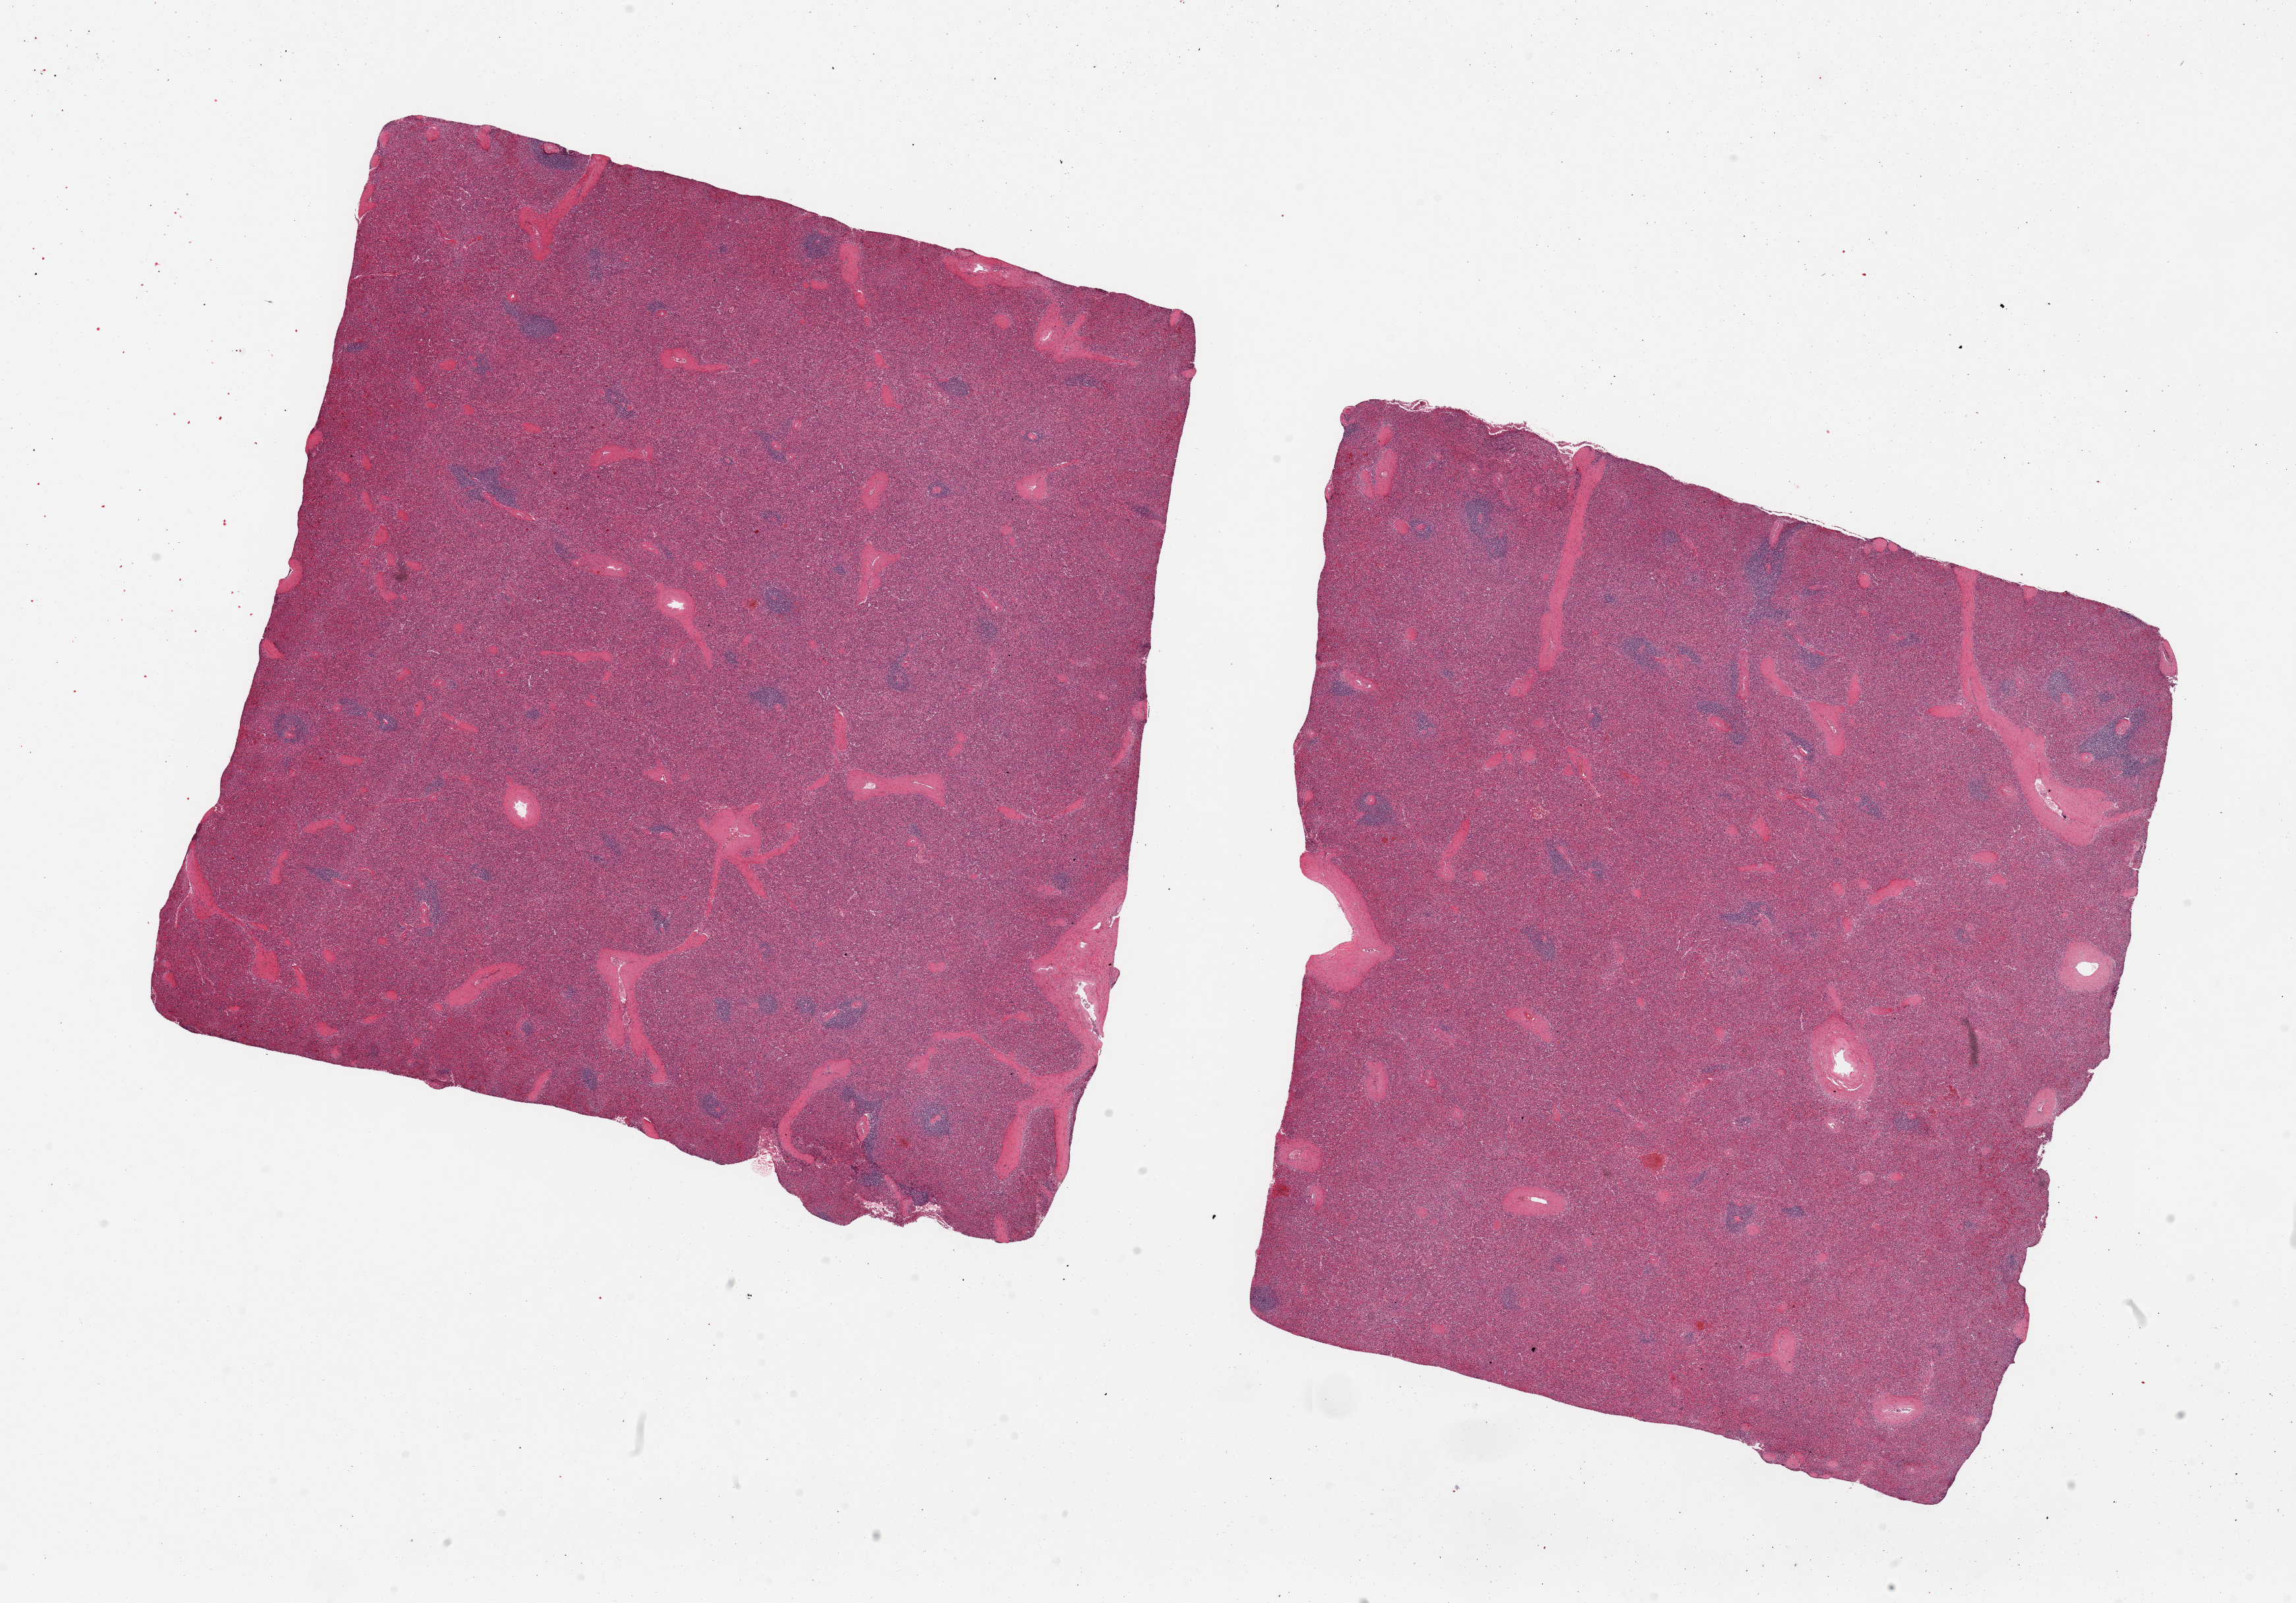
Digitized haematoxylin and eosin-stained section, a low-resolution overview of the entire scanned area, about 27.6 x 19.2 mm. PAXgene-fixed paraffin-embedded (PFPE) section. Target tissue: spleen. Tissue donor sample. Male donor.
Review note (as recorded): 2 pieces; not congested; white pulp (lymphoid tissue) depleted.